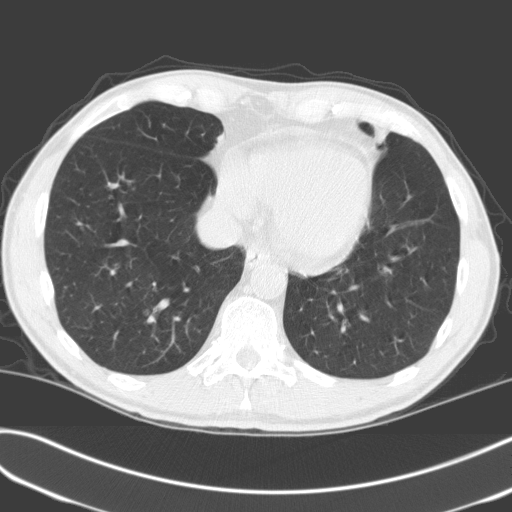
Low-dose screening chest CT, one axial slice. Position 52 of 170 along the scan axis. 120 kVp. Lung window (W 1500 / L -600 HU). 3.2 mm slice thickness. 512 × 512 image matrix.
Annotated regions visible in this slice (outlined manually by an expert reader):
- lesion 1 (tumor, upper lobe of left lung): bounding box [x1, y1, x2, y2] px = [372, 125, 389, 144]